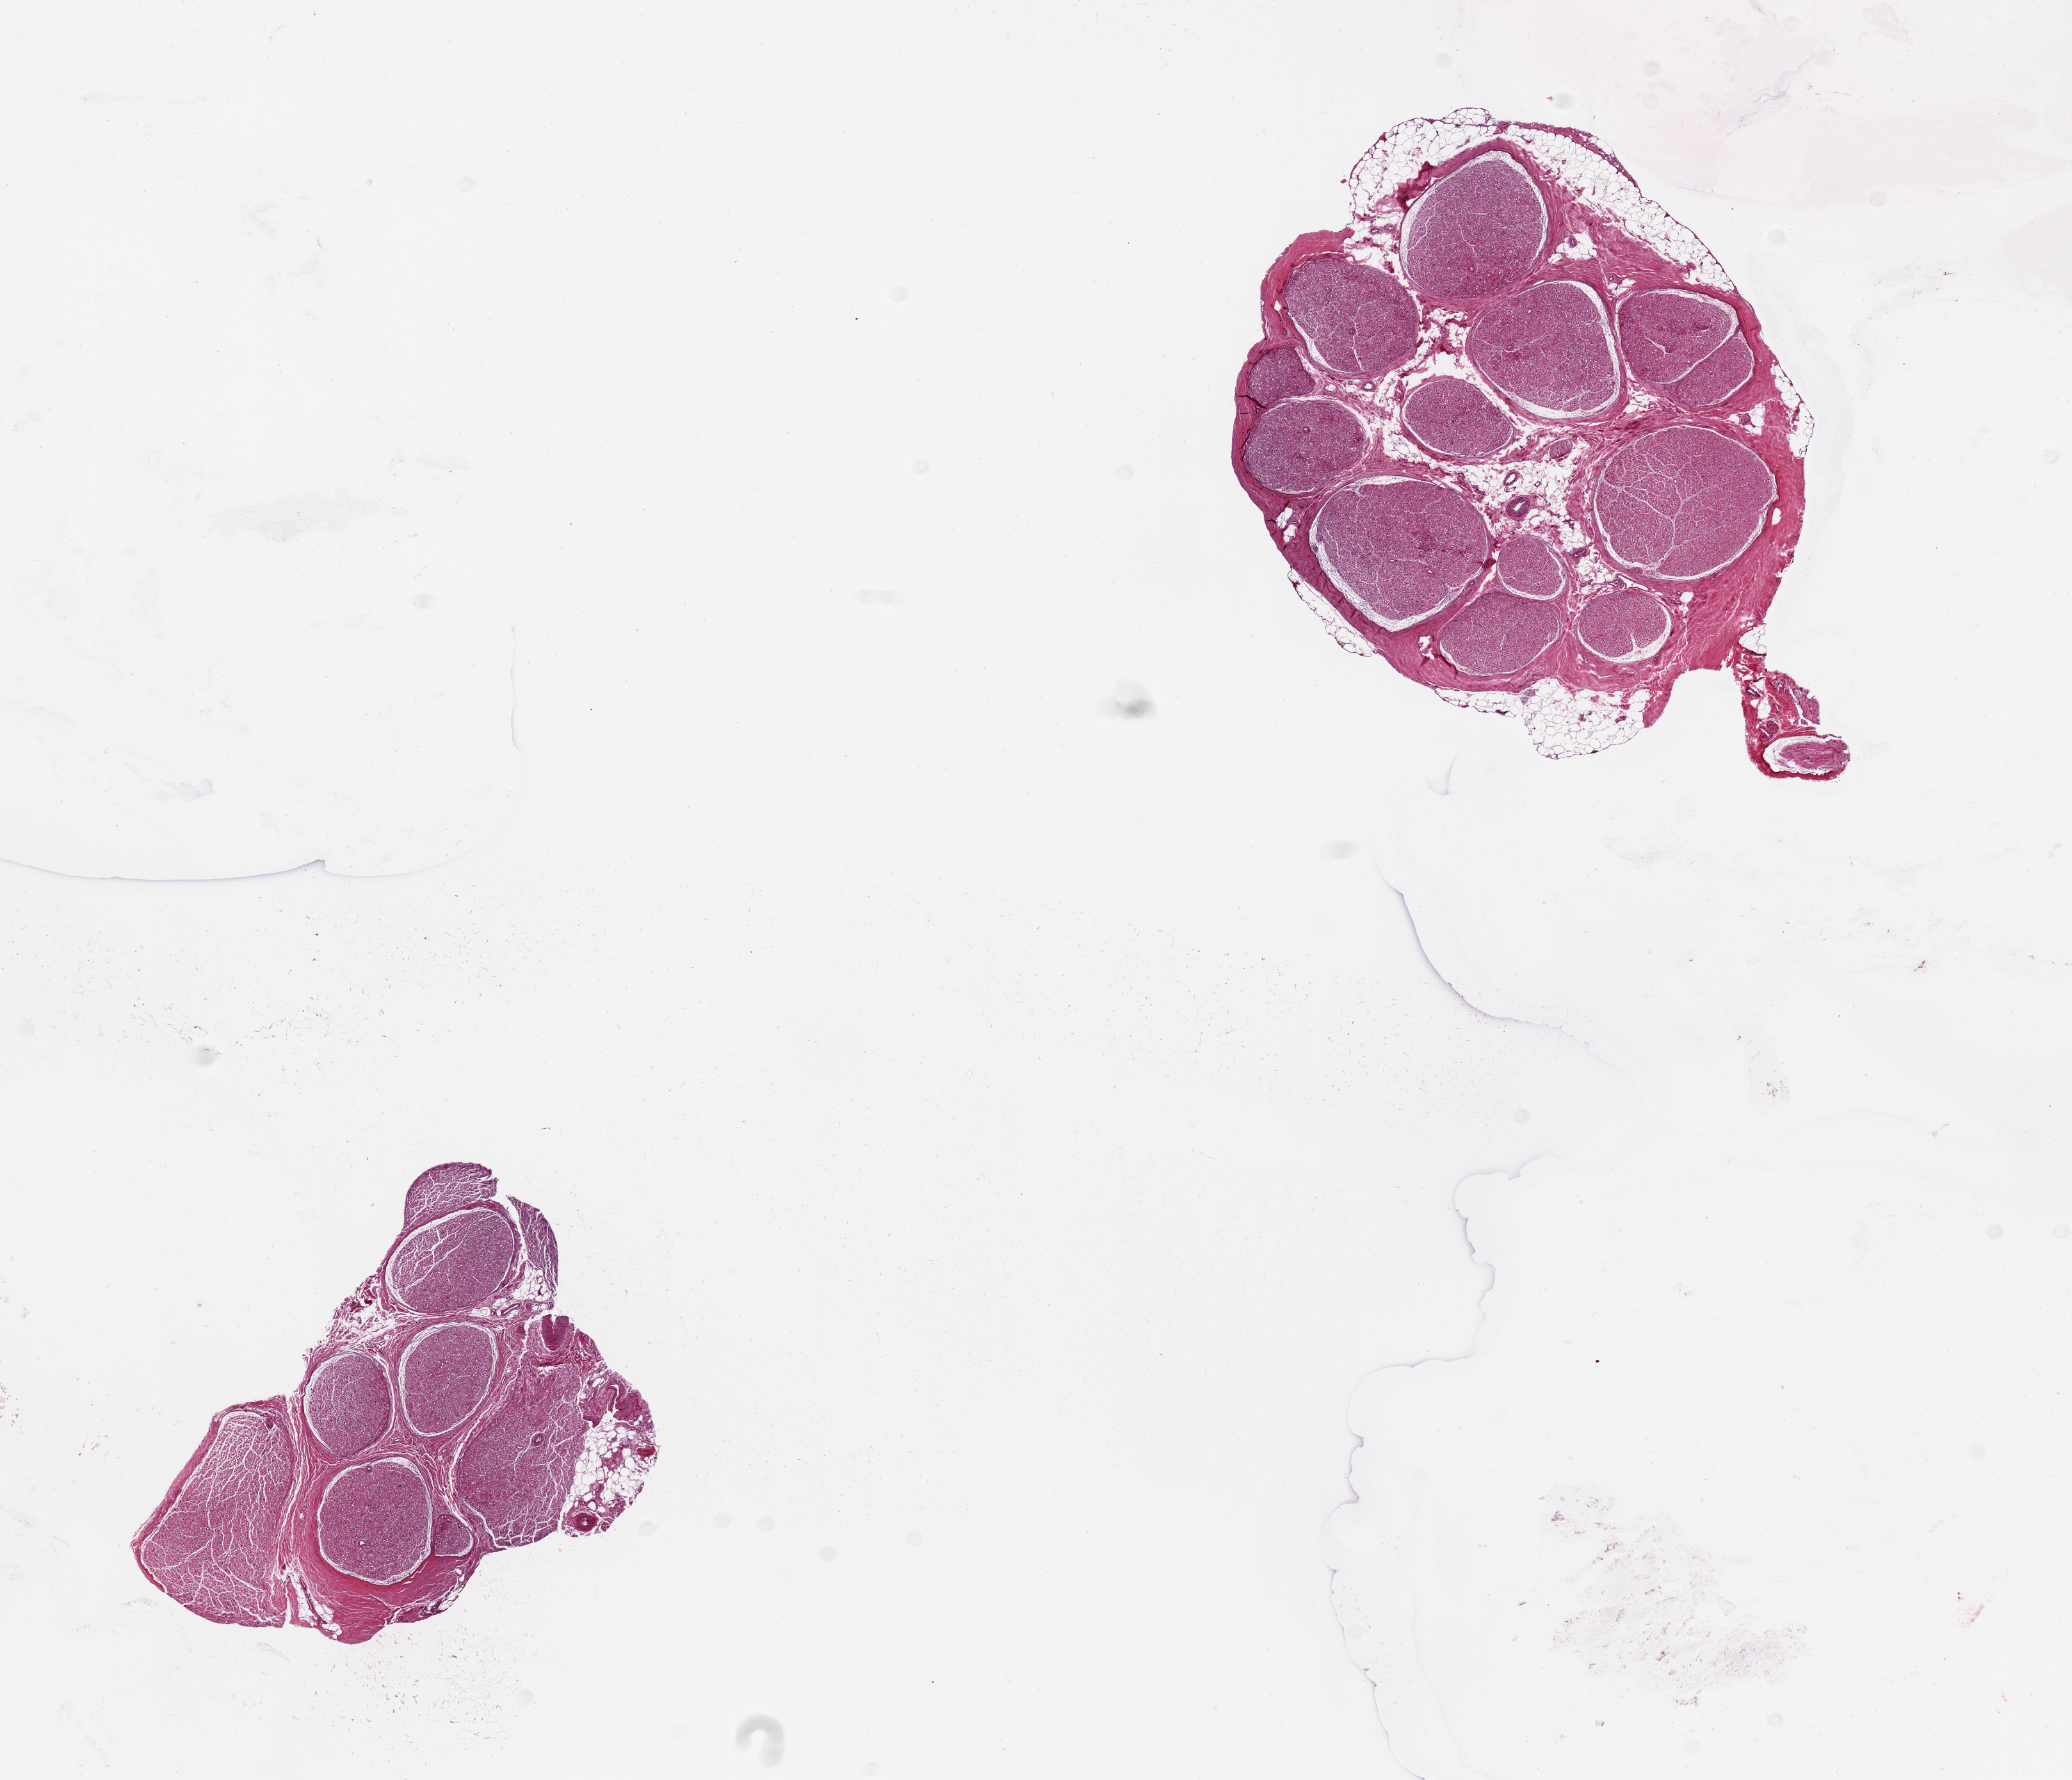
Whole-slide image, H&E stain, shown as a low-resolution overview of the whole scanned area (about 12.8 x 11.0 mm, slide scanned at 20x); PAXgene-fixed, paraffin-embedded tissue; target tissue: tibial nerve; donor tissue sample. Donor: male.
Reviewer comment on this tissue sample: 2 pieces; small amount of attached and internal fat (up to 10-15%).